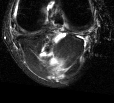
MRI of an extremity soft-tissue mass, one axial slice; slice 10 of 44 in the series (ordered by position); T2-weighted fat-saturated; MR volume resampled by the dataset authors to the PET/CT grid (not the native acquisition matrix); 3.27 mm slice thickness; 114 × 103 image matrix, field of view 111 × 101 mm. Female patient. Case-level facts recorded for this patient, not image findings: histological type: liposarcoma; site of the primary tumour: right thigh.
Outlined on this slice (expert contour drawn on MRI and transferred to this co-registered scan by the dataset authors):
- gross tumour volume (mass): box from (x=45, y=55) to (x=66, y=74) px